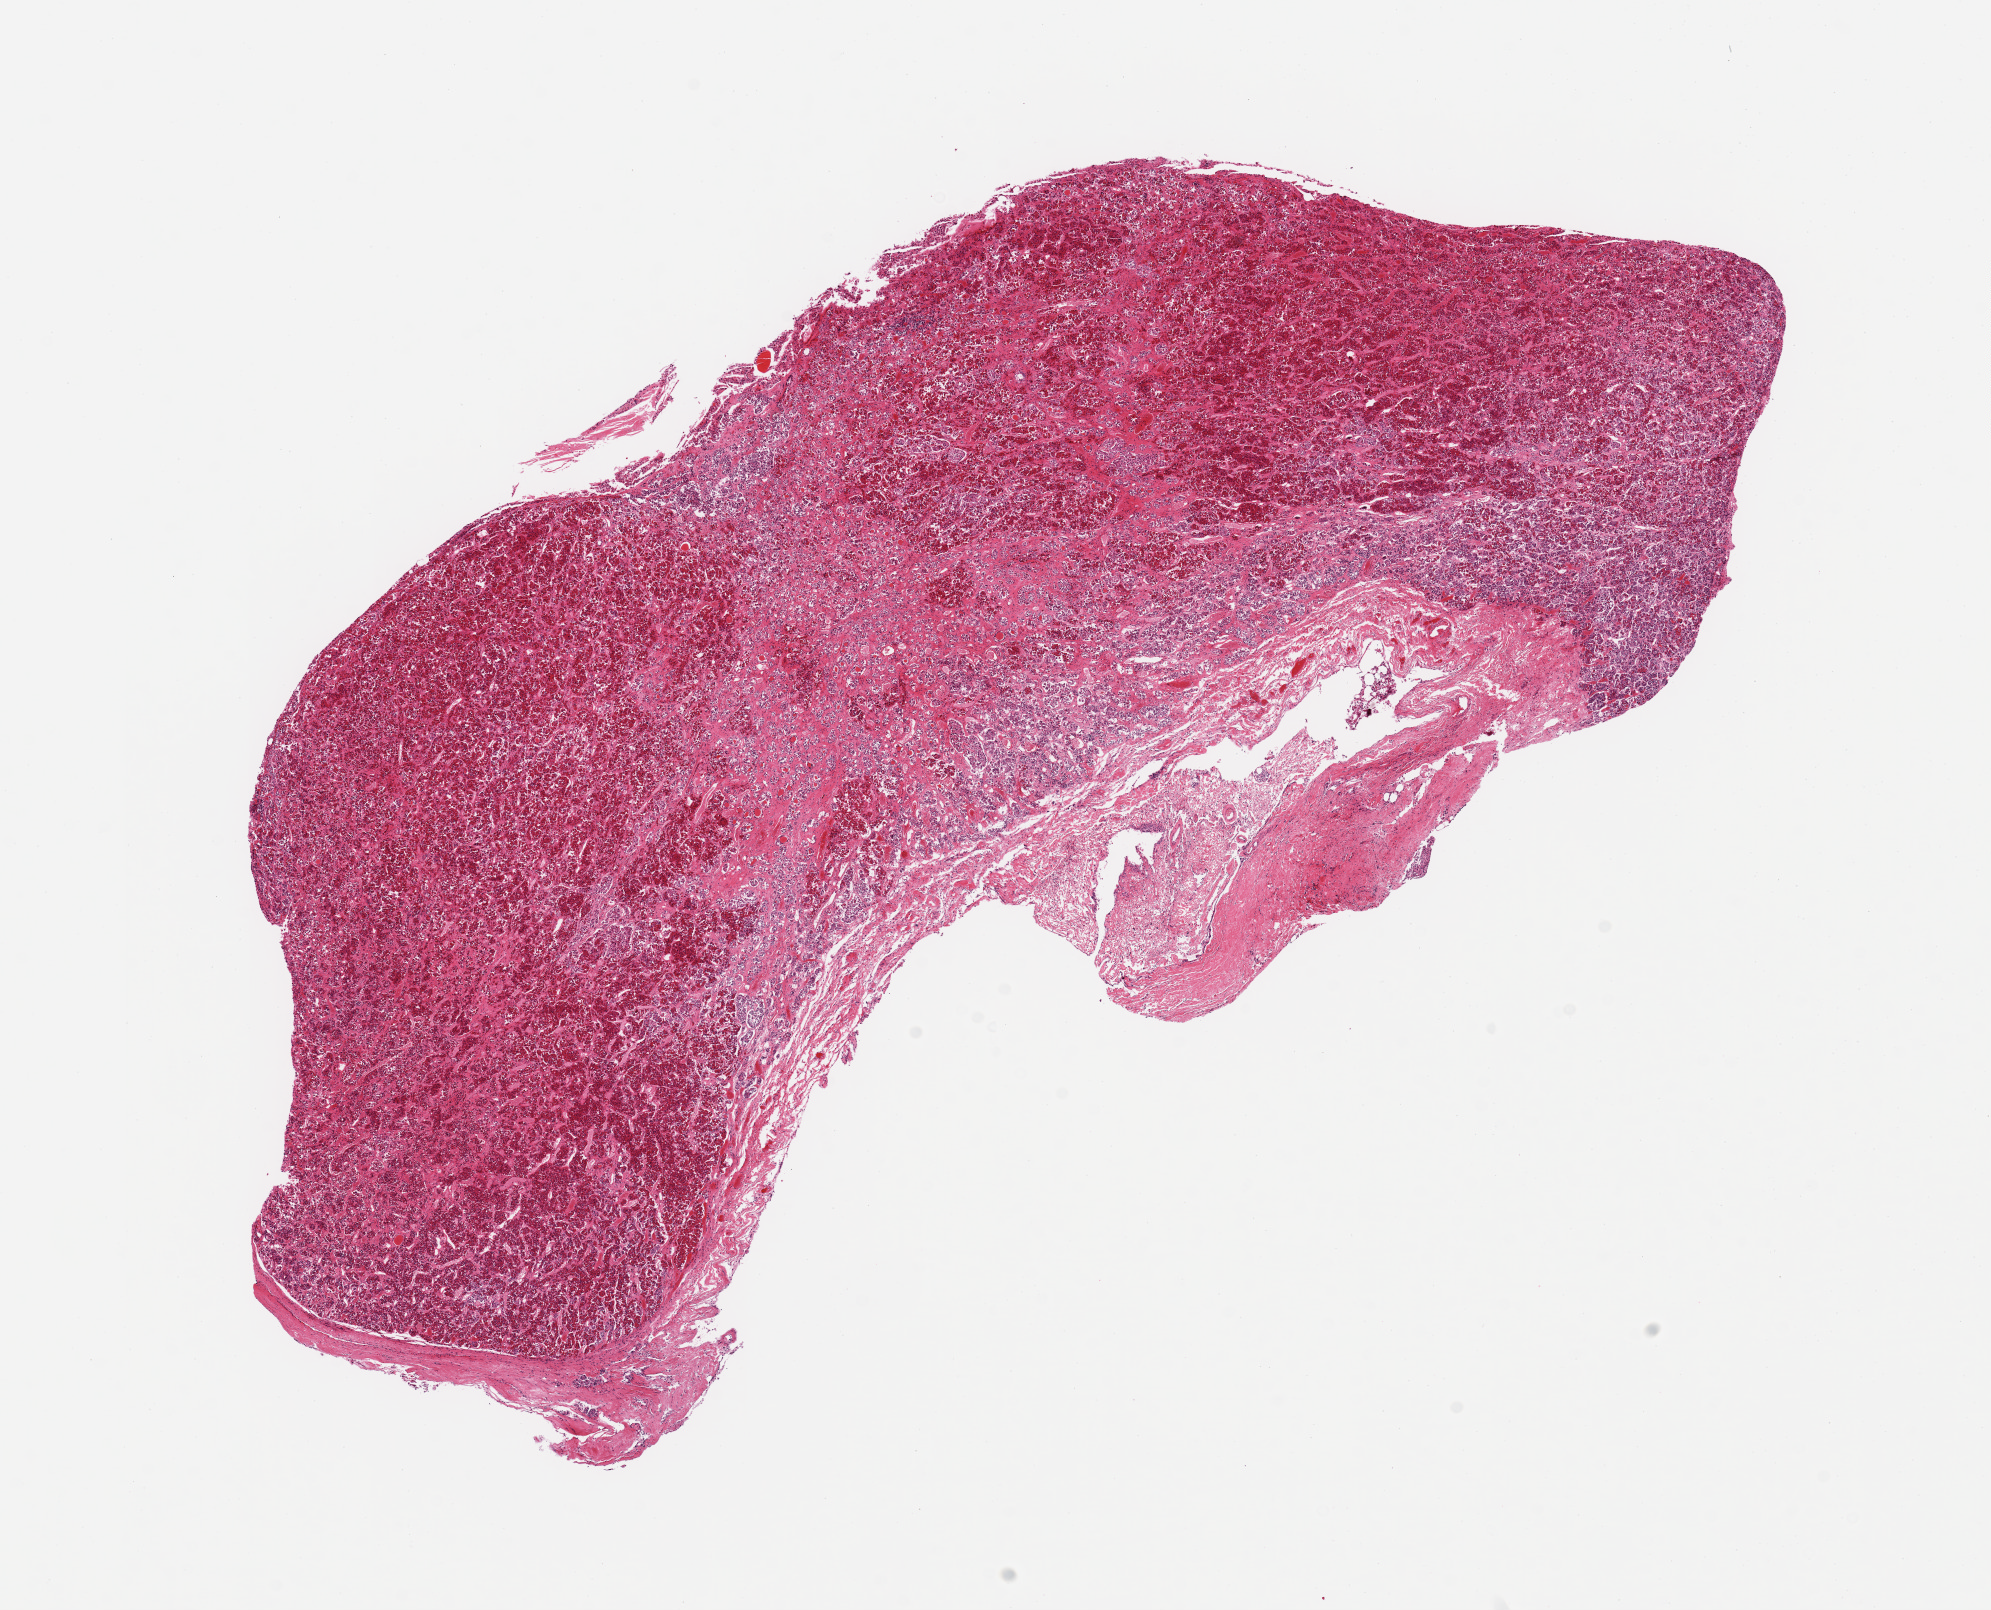
Digitized hematoxylin and eosin (H&E)-stained section, brightfield — whole scanned area (about 15.8 x 12.7 mm, from a 20x scan) shown as a low-resolution overview, PAXgene-fixed paraffin-embedded (PFPE) section, section of pituitary (target tissue), tissue donor sample. Male donor.
• reviewer comment on this tissue sample: 1 piece; adenohypophysis, no neural component